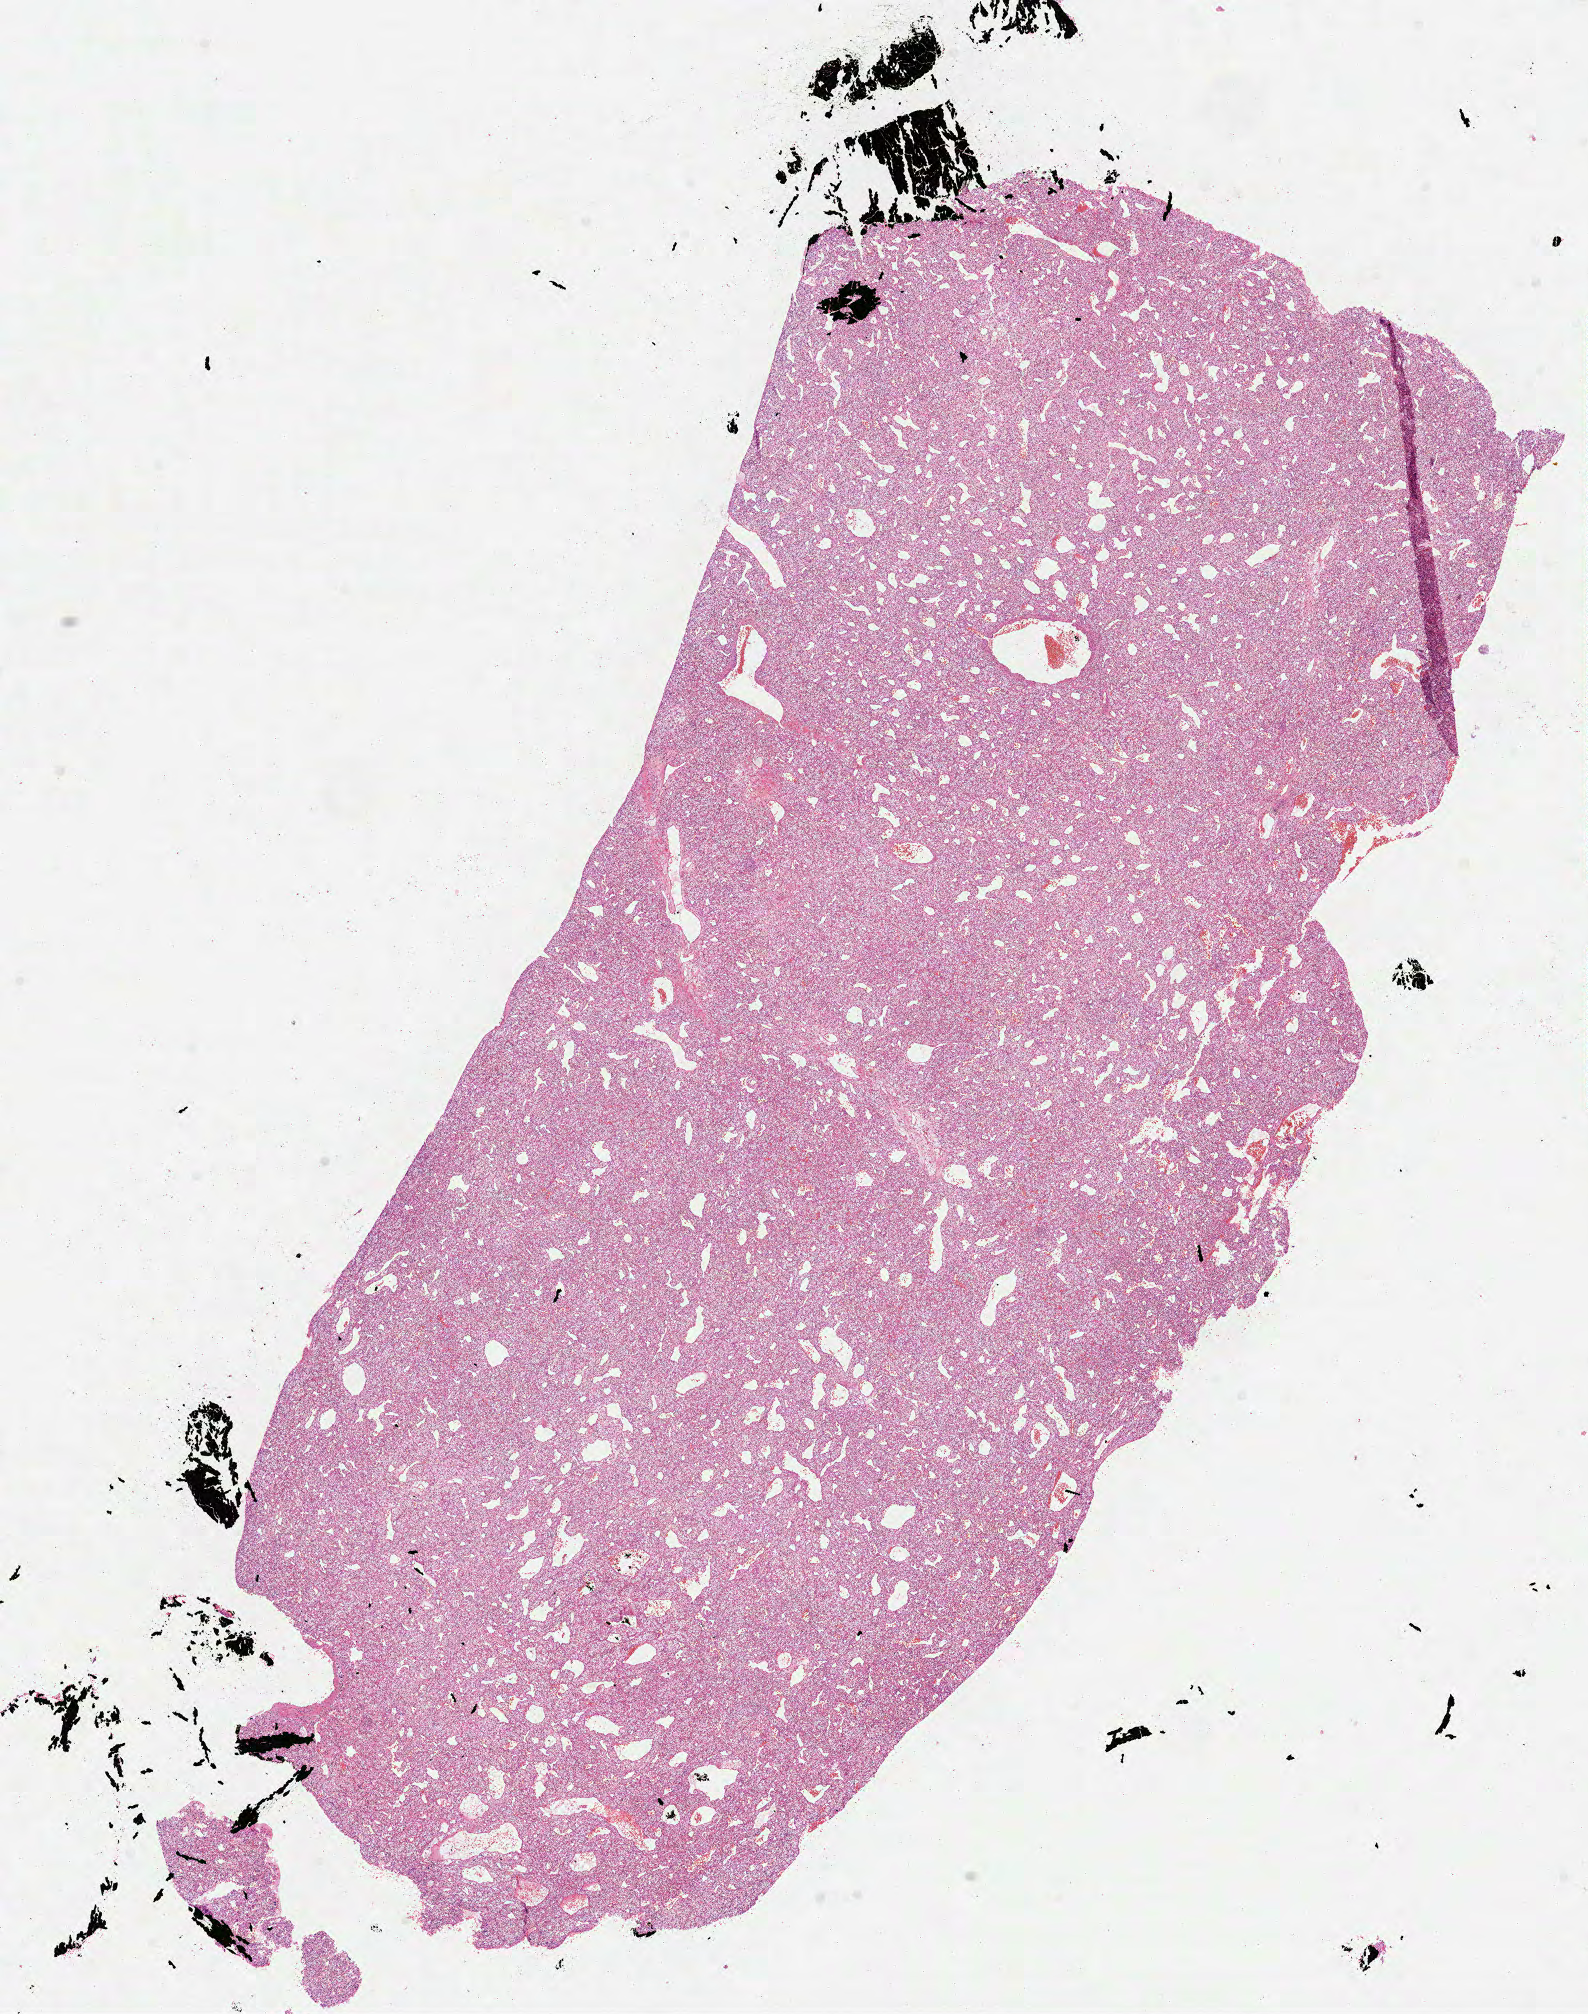
Hematoxylin and eosin (H&E) stained whole-slide image, a low-resolution overview of the entire scanned area, about 12.8 x 16.2 mm (acquisition: 40x scan), formalin-fixed paraffin-embedded (FFPE) diagnostic section, sample: primary tumour, kidney. Male patient; age at initial diagnosis 75 years. Histologic grade: G2 (moderately differentiated).
• AJCC pathologic stage: I
• histologic diagnosis: Clear cell adenocarcinoma, NOS
• laterality: right